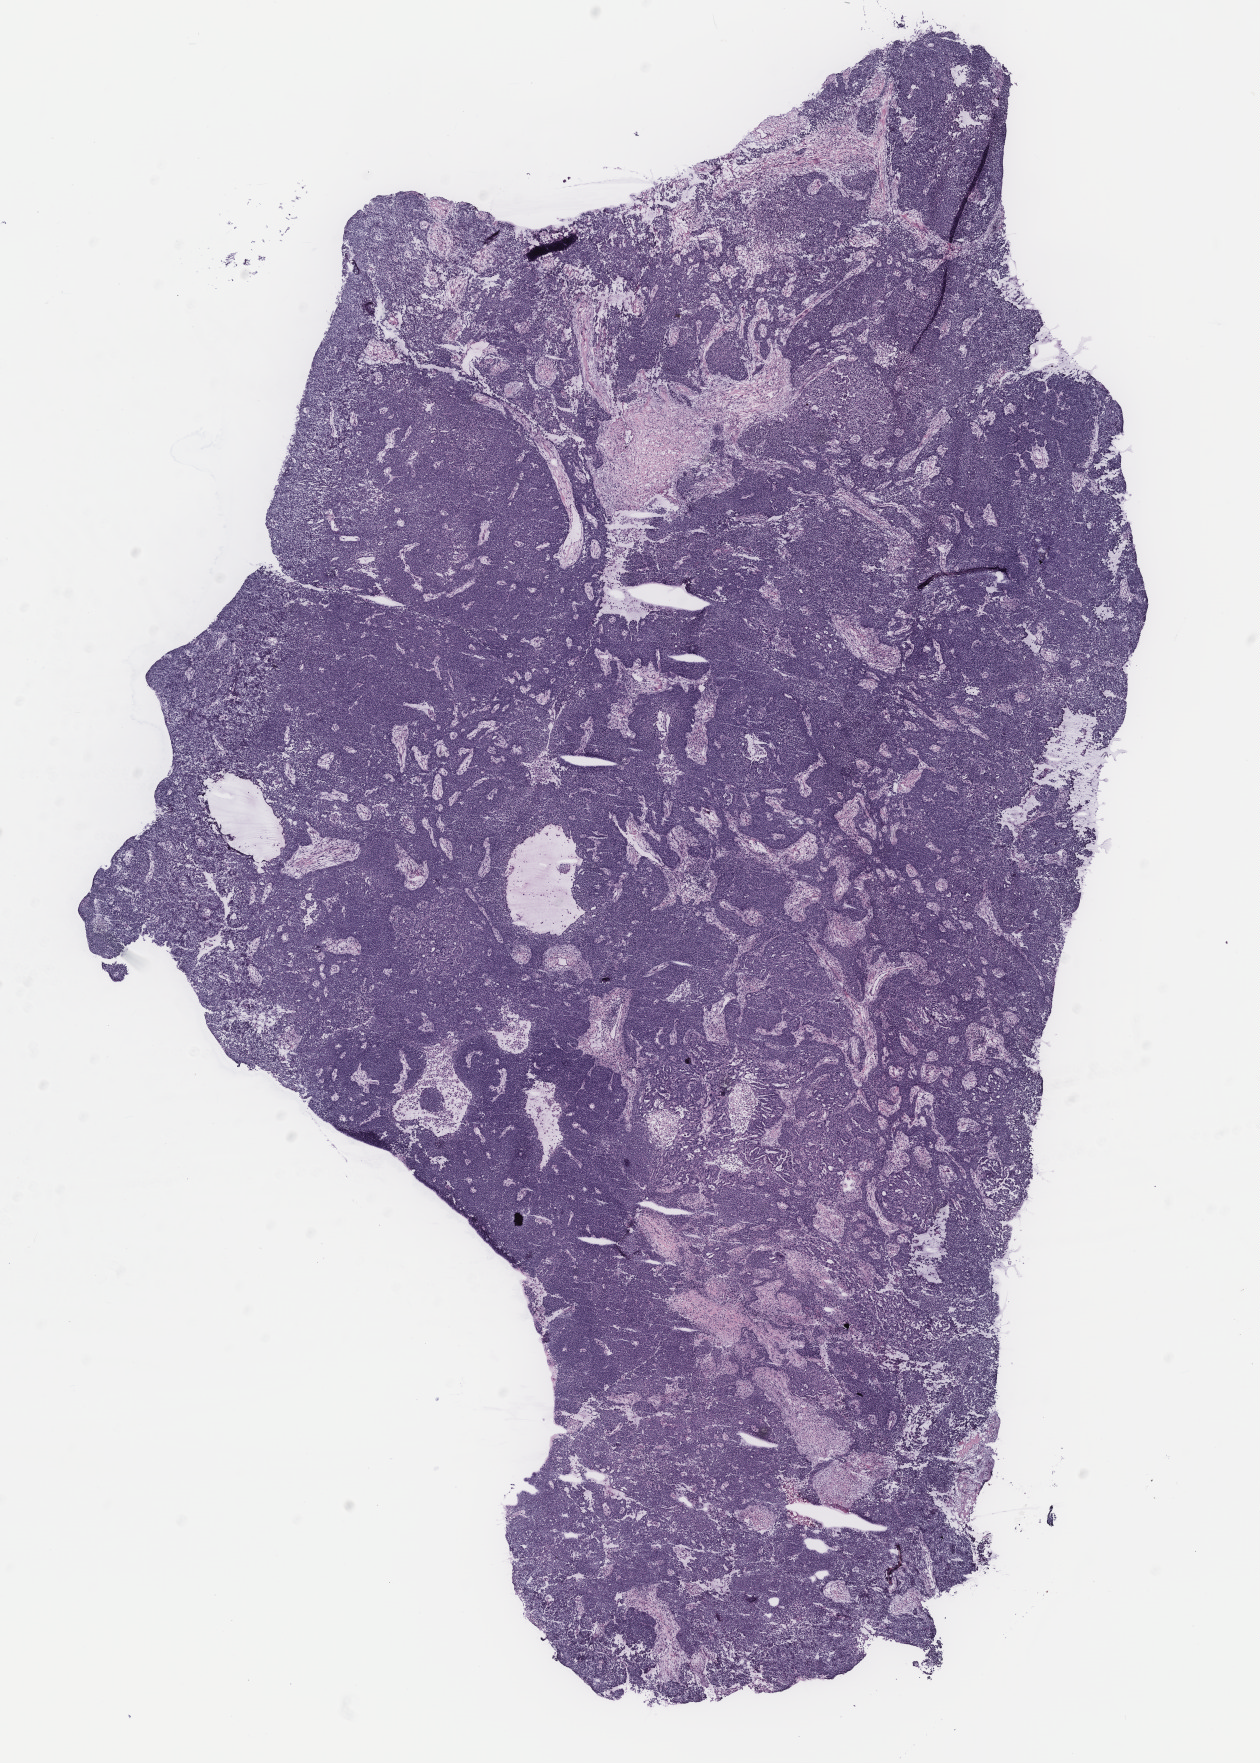
Whole-slide histology image, H&E, whole scanned area (about 10.1 x 14.1 mm) shown as a low-resolution overview; tumour tissue sample, ovary. 54-year-old female patient.
Diagnosis: Serous adenocarcinoma, NOS (peritoneum, NOS).